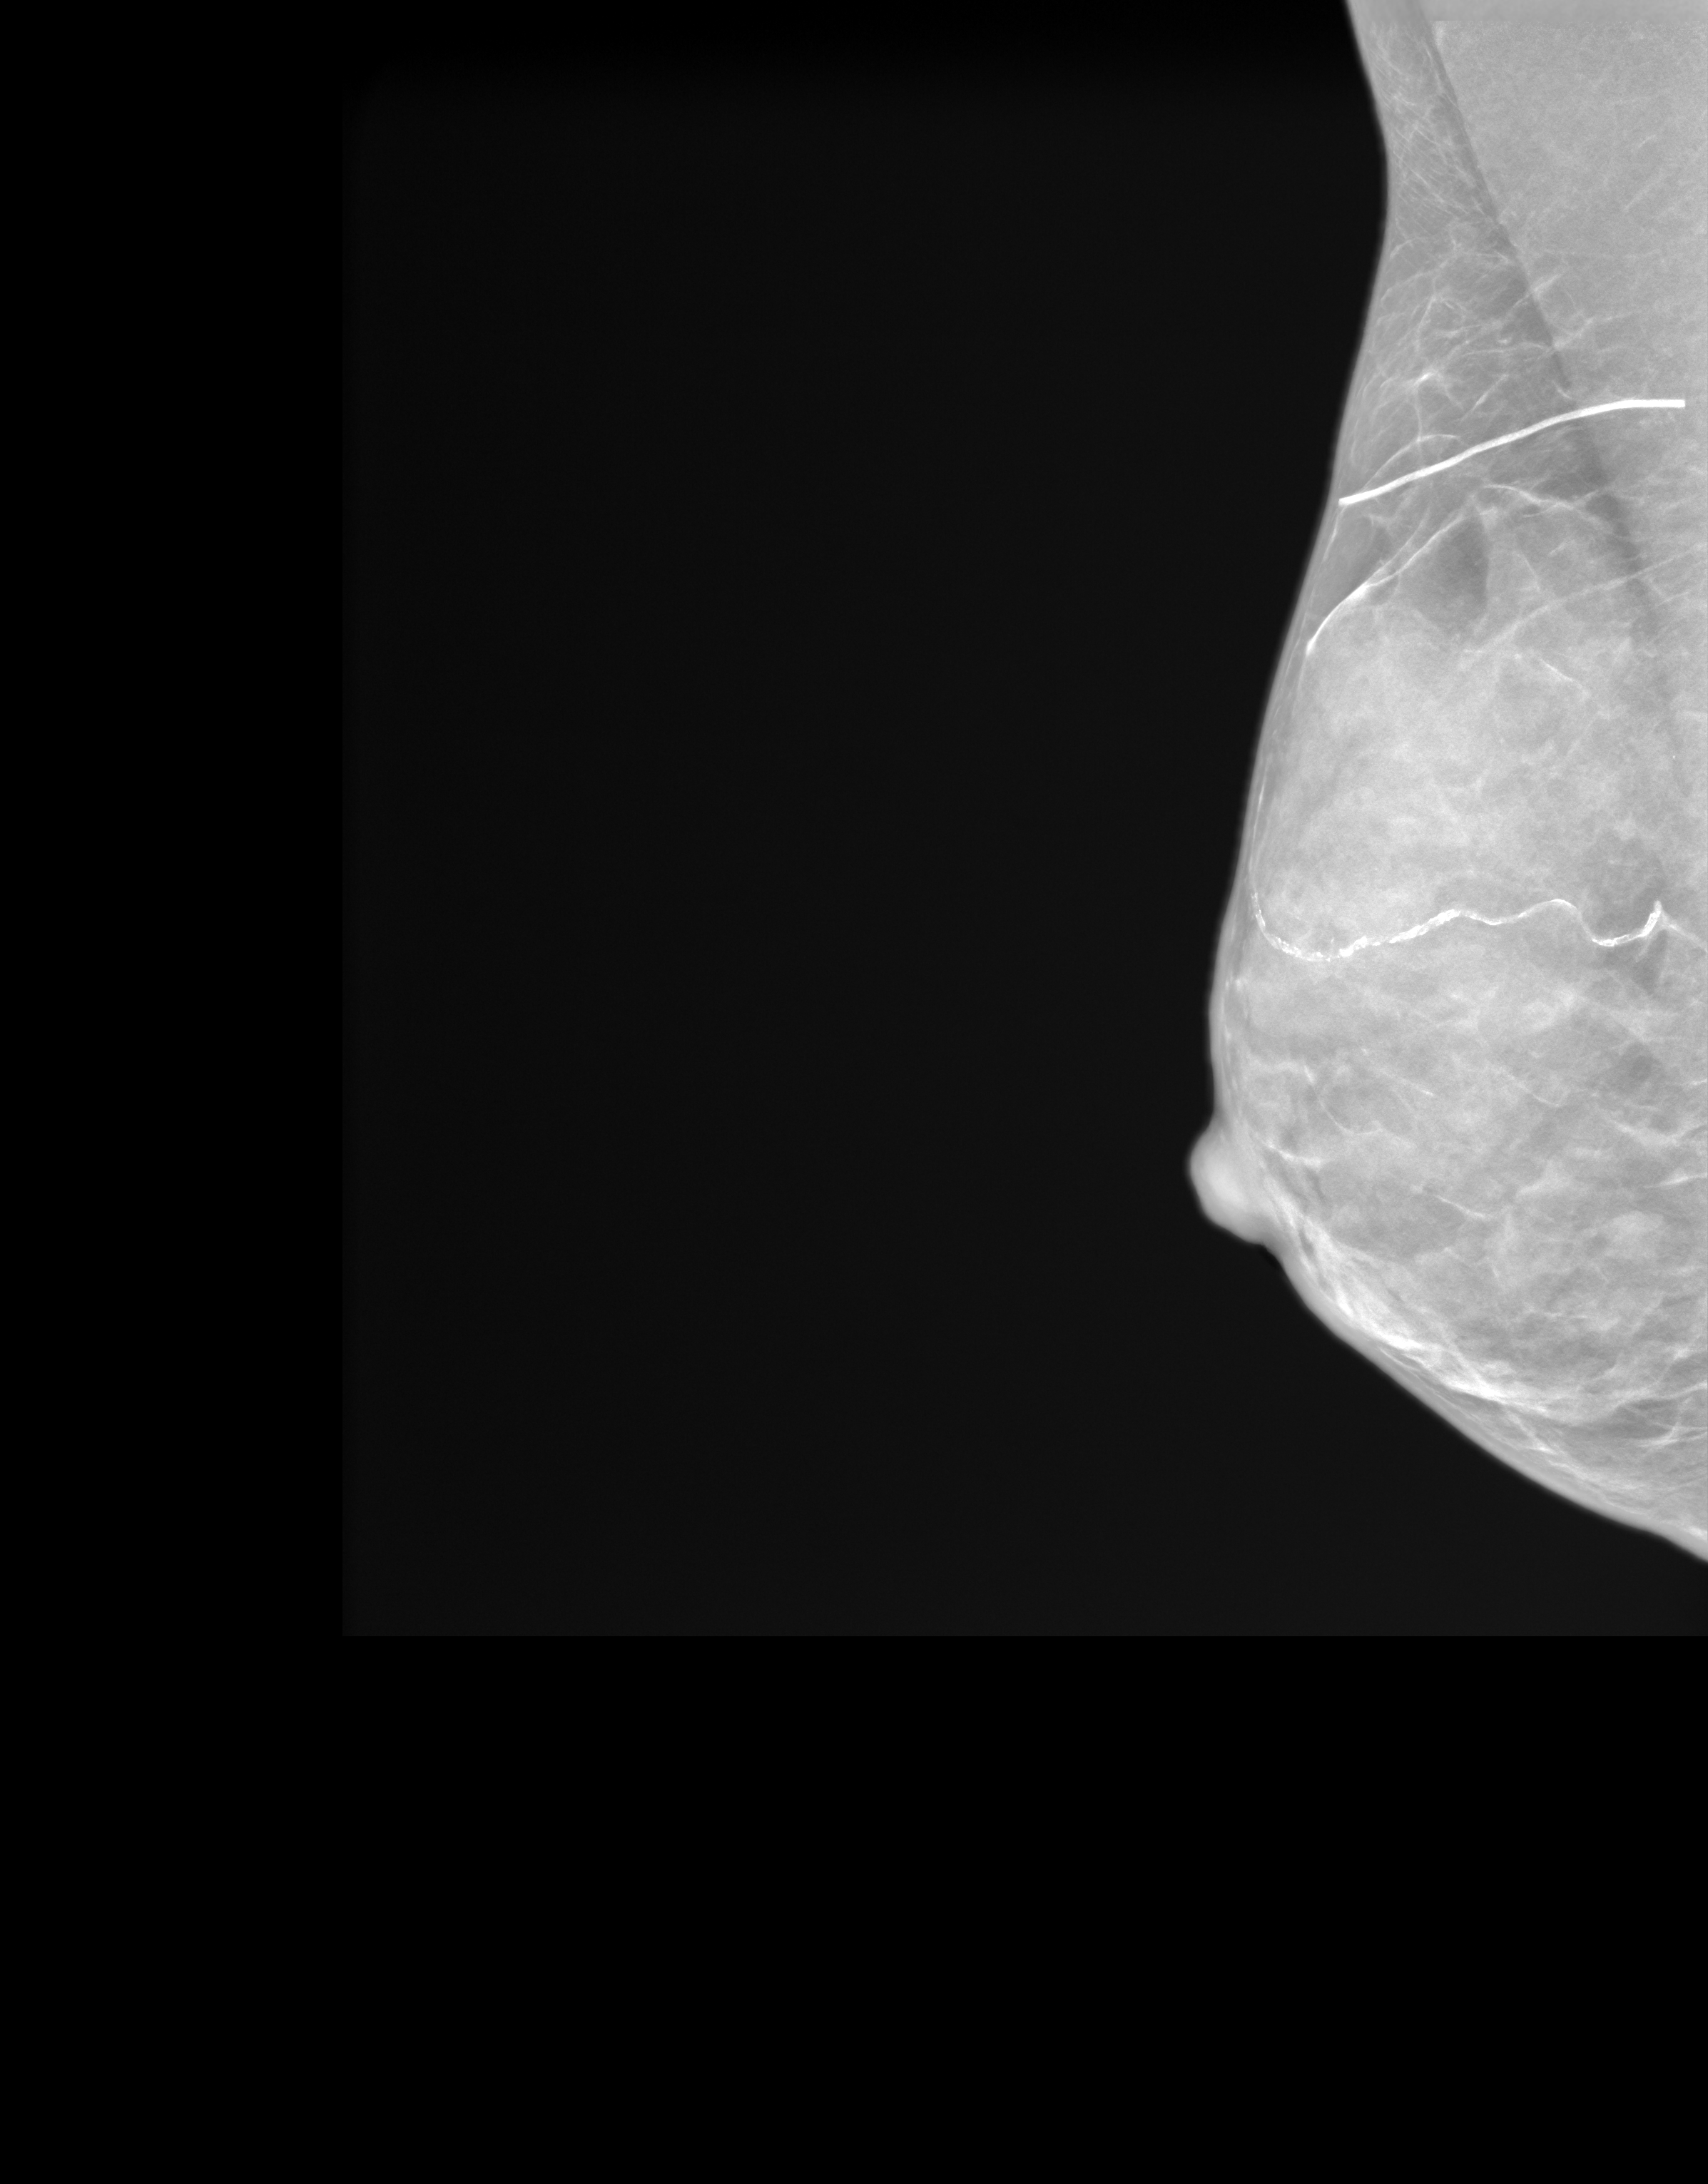
Screening examination; system: SenoIris_1SP1.1(421). Patient: female, 59 years.
Image type: synthesized 2-D view from tomosynthesis. Breast: right. Projection: mediolateral oblique (MLO) view.